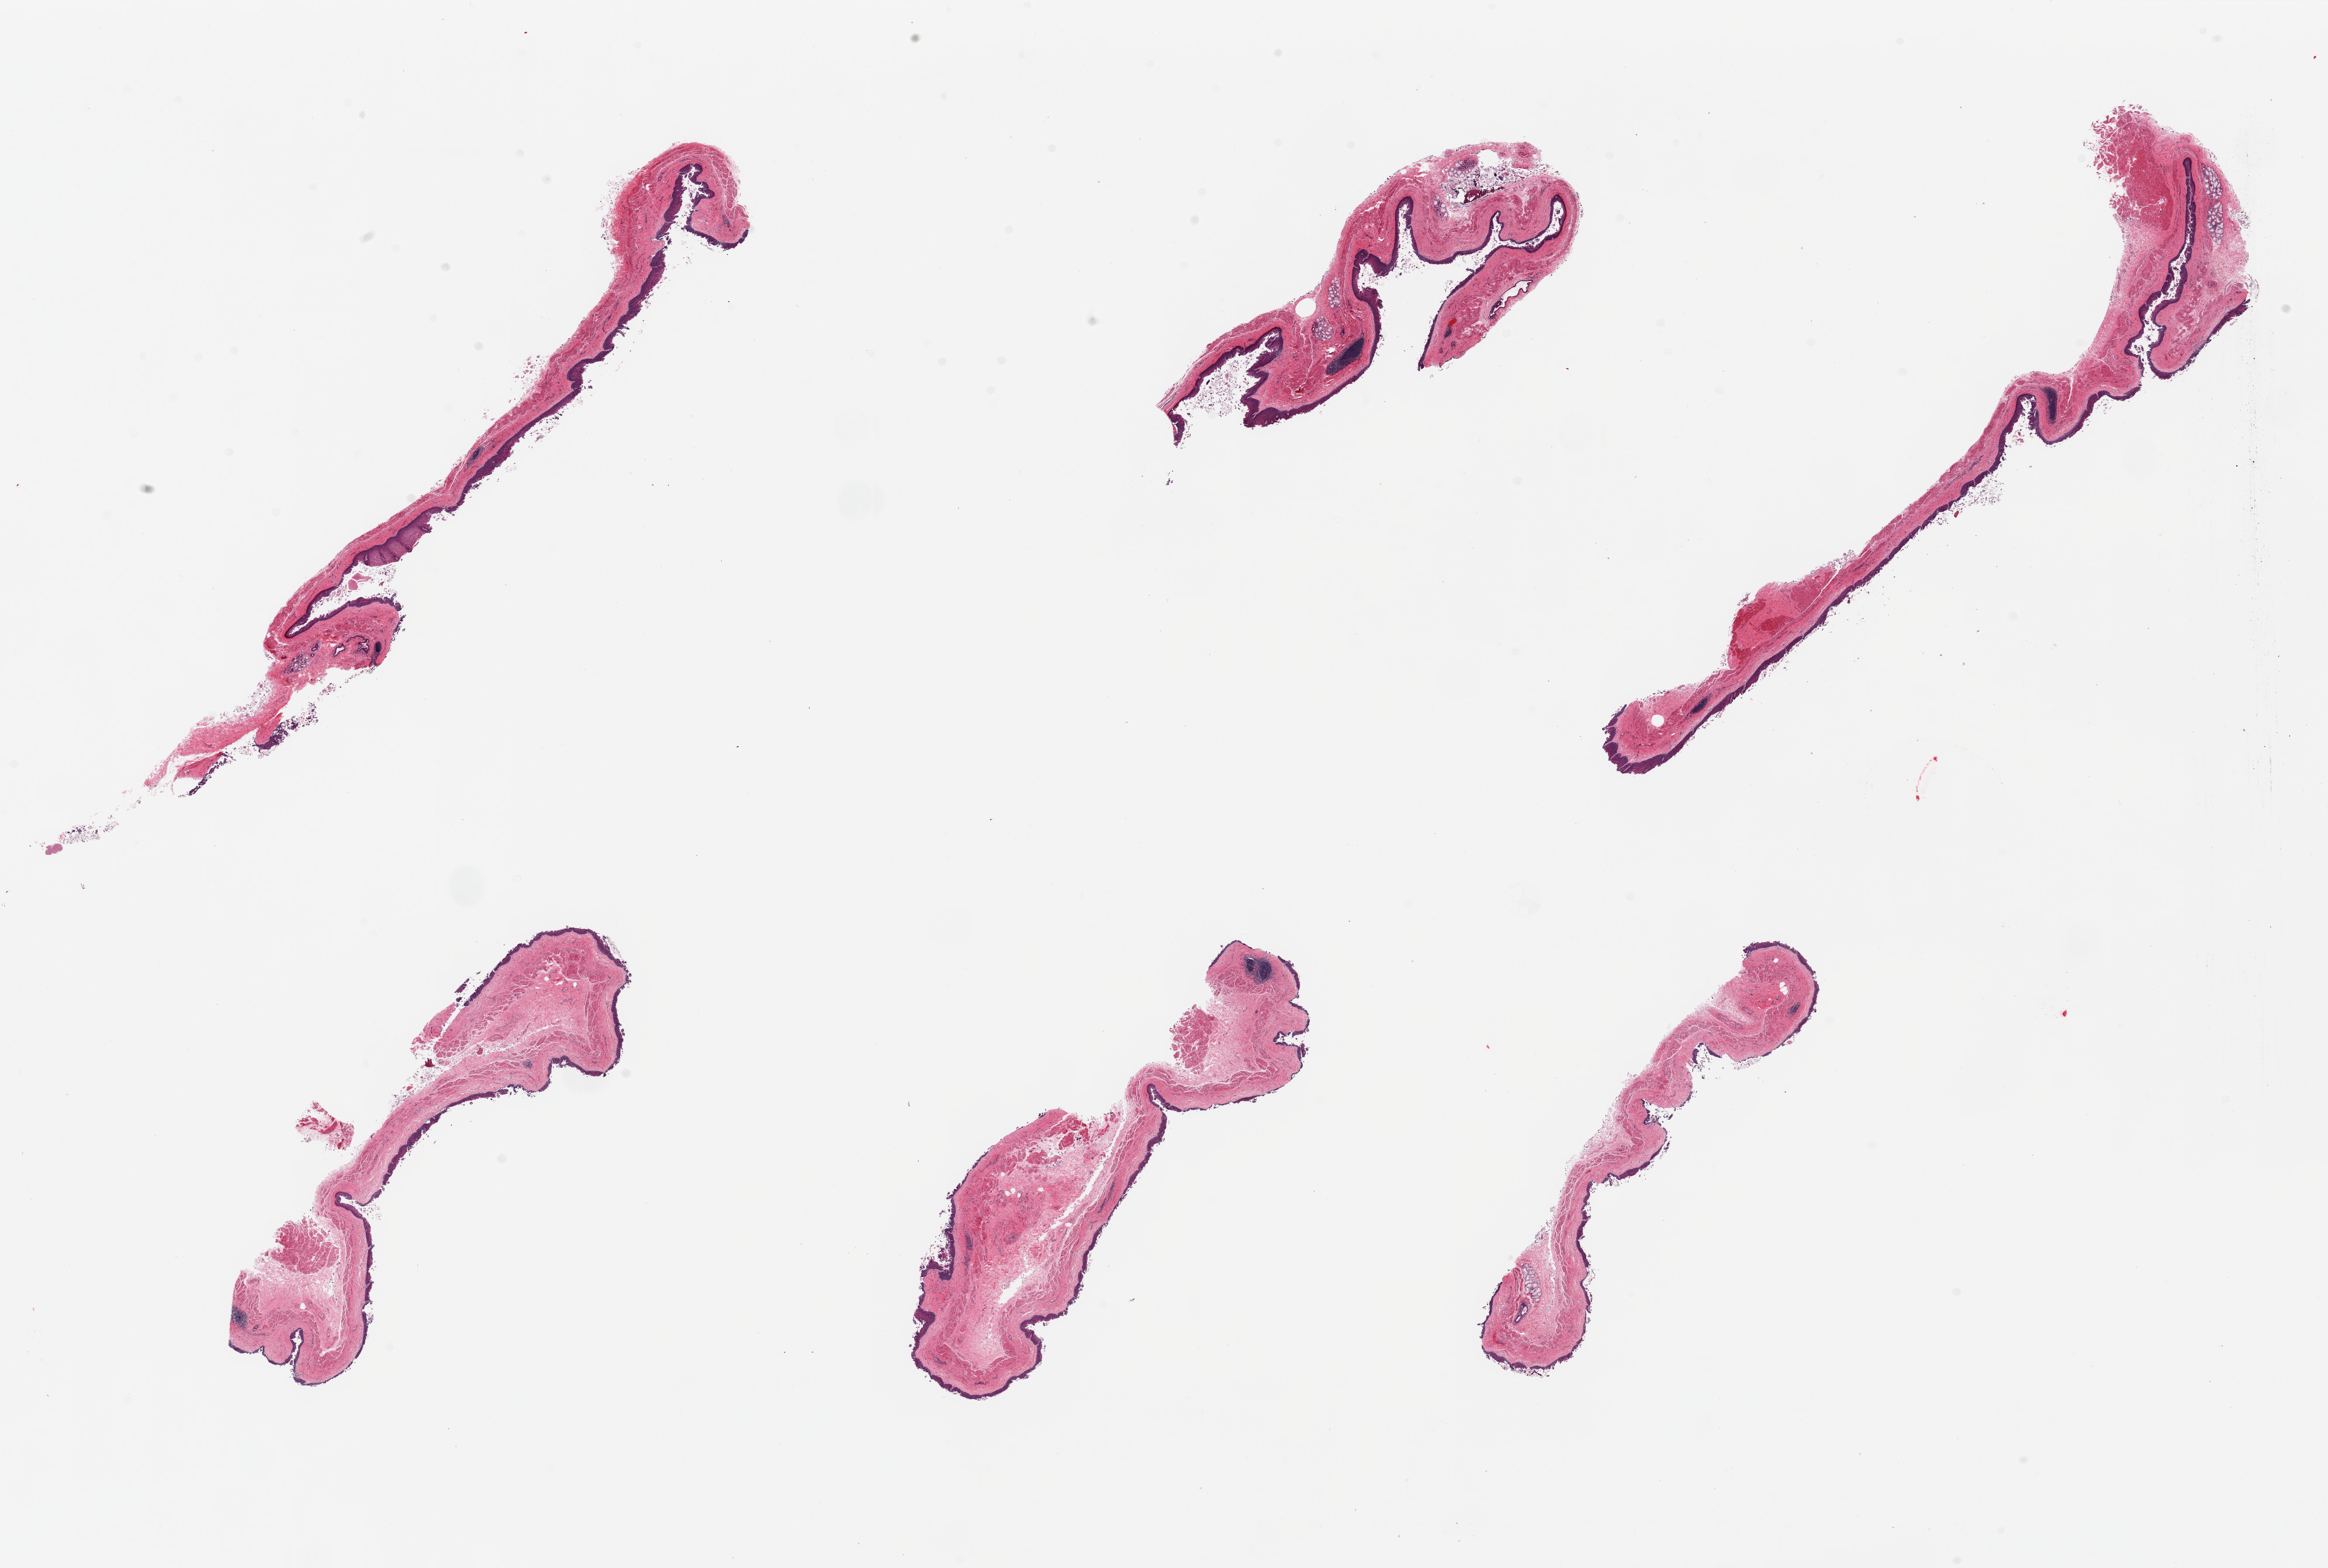
Whole-slide image, H&E stain, brightfield — low-resolution overview of the scanned area, about 31.5 x 21.2 mm, PAXgene-fixed paraffin-embedded (PFPE) section, target tissue: esophageal mucous membrane, tissue donor sample.
Reviewer comment on this tissue sample: 6 pieces; few strips include small portion of muscularis, epithelium sloughing, few lymphoid aggregates, rare dilated submucosal gland (pseudodiverticulosis).